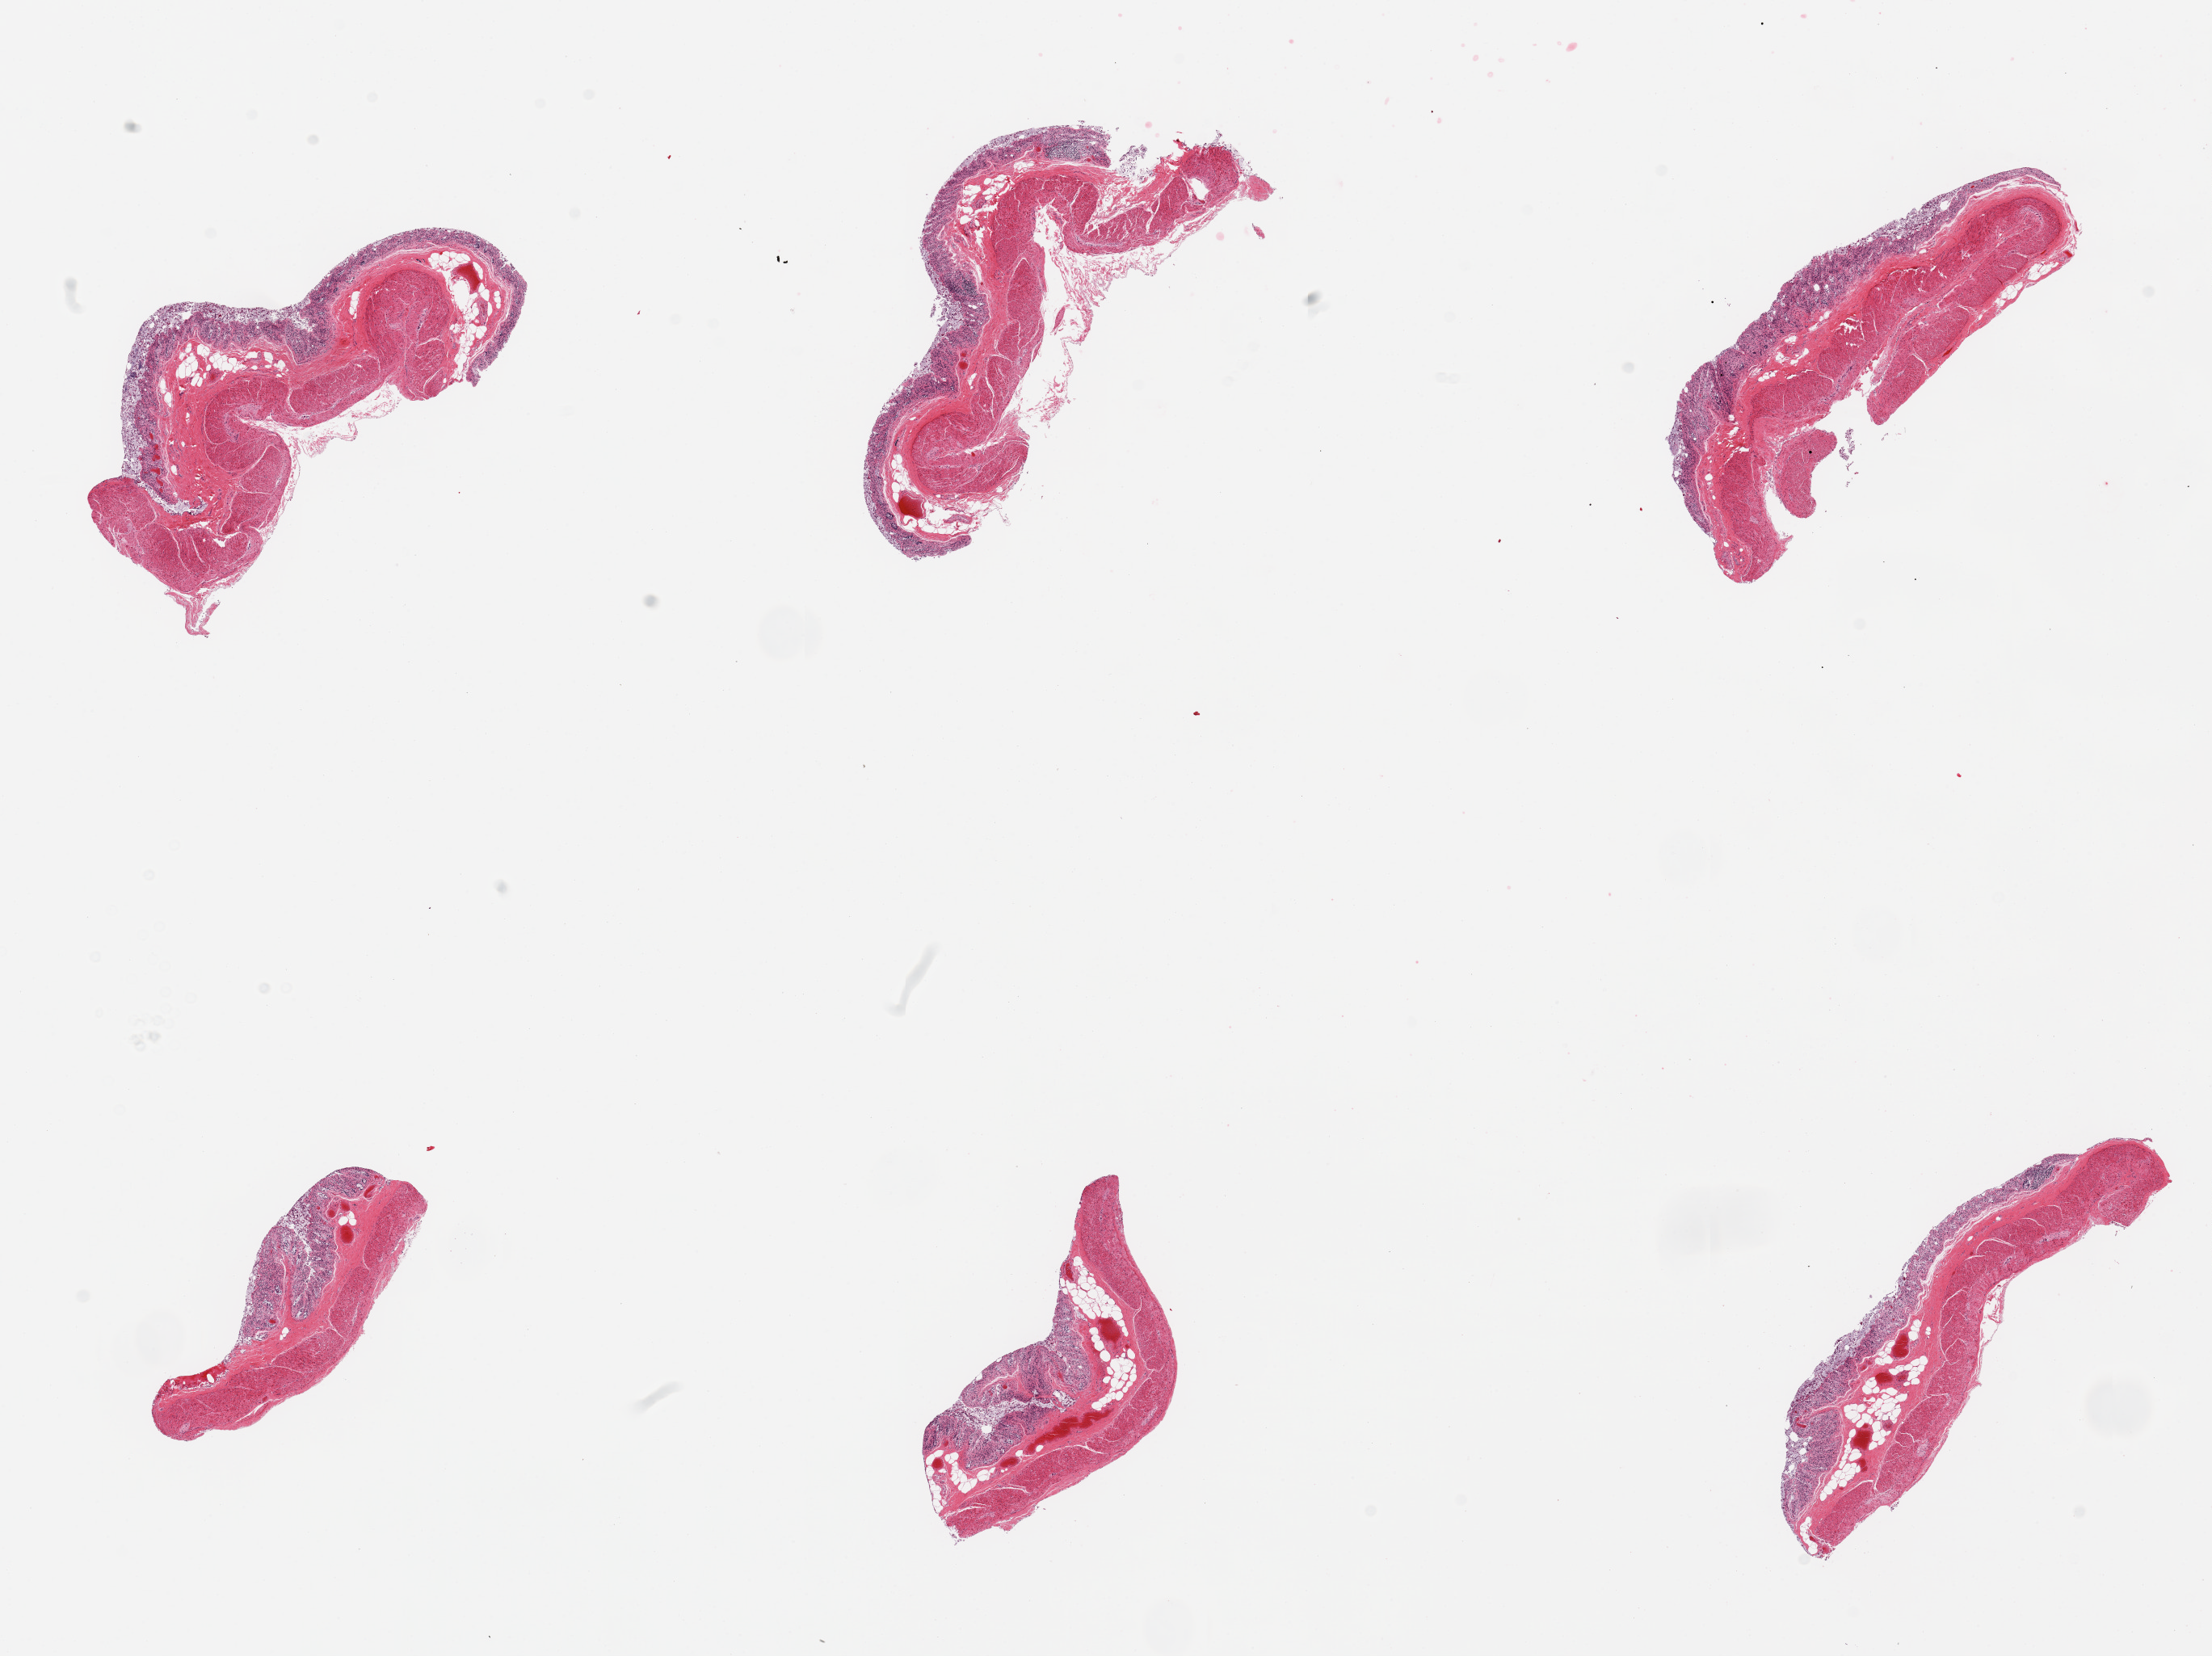
Whole-slide image, haematoxylin and eosin stain, brightfield — whole scanned area (about 21.7 x 16.2 mm, from a 20x scan) shown as a low-resolution overview. PAXgene-fixed, paraffin-embedded tissue. Section of transverse colon (target tissue). Donor tissue sample.
Review note (as recorded): 6 pieces; full thickness sections, mucosa (3), muscularis (2).